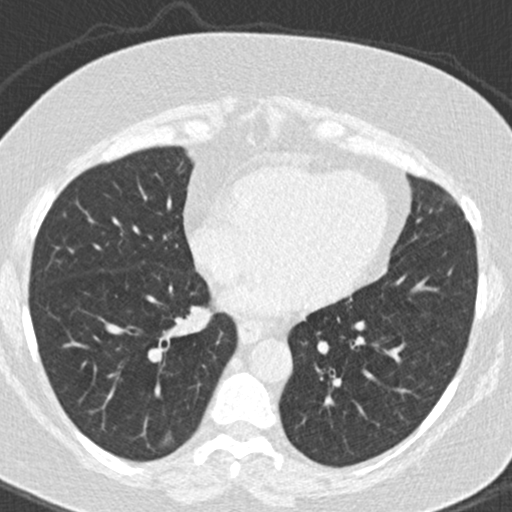
Chest CT (low-dose screening protocol), one axial image. Baseline screening round. Lung window (W 1500 / L -600 HU). 2 mm slice thickness. 120 kVp. Female participant, aged 63 years at enrolment. Former smoker at enrolment.
Expert reader's lesion annotation, bounding box (x1, y1, x2, y2) in pixels: (148, 419, 186, 459). The exam's reader record, not a measurement of the box and not confirmed to be the same lesion: non-calcified nodule or mass ≥4 mm, right lower lobe, 16 × 10 mm, poorly defined margins, ground glass attenuation. Official screen result: positive, change unspecified: nodule(s) >= 4 mm or enlarging nodule(s), mass(es), or other non-specific abnormalities suspicious for lung cancer. Lung cancer was diagnosed 246 days after this screen: bronchiolo-alveolar adenocarcinoma, NOS, right lower lobe, well differentiated (G1), stage IA (AJCC 6th edition), 12 mm at pathology.